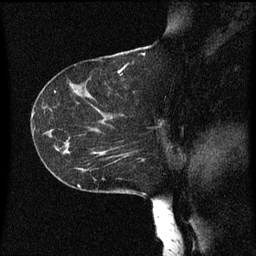
Breast MRI (dynamic contrast-enhanced), one sagittal slice; position 35 of 60 along the scan axis; dynamic contrast-enhanced series, image 2 of 3 at this slice position (ordered by acquisition); 1.5 T; TE 4.2 ms, TR 8 ms; 2 mm slice thickness; 256 × 256 image matrix, field of view 200 × 200 mm. Patient: female, 55 years.
Outlined on this slice (semi-automatically segmented with operator editing):
- analysis volume of interest (the breast-tissue region the enhancement analysis was run in; not a lesion): box from (x=46, y=124) to (x=151, y=183) px
- tumour enhancement mask (voxels above the 70 % enhancement threshold inside the analysis volume of interest): (x=96, y=152)–(x=145, y=161)